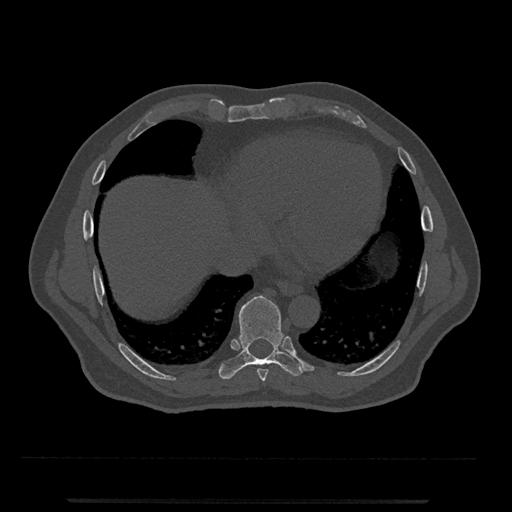
CT including the spine, one axial slice; slice 587 of 797 in the series (ordered by position); 120 kVp; bone window (W 1800 / L 400 HU); 512 × 512 image matrix. Male patient, age 63 years. Case-level facts recorded for this patient, not image findings: primary cancer: prostate.
Structures marked on this image (semi-automatic segmentation, software-assisted and operator-edited):
- T8 vertebra: bounding box (x1, y1, x2, y2) in pixels: (257, 369, 268, 382)
- T9 vertebra: (219, 295, 305, 379)